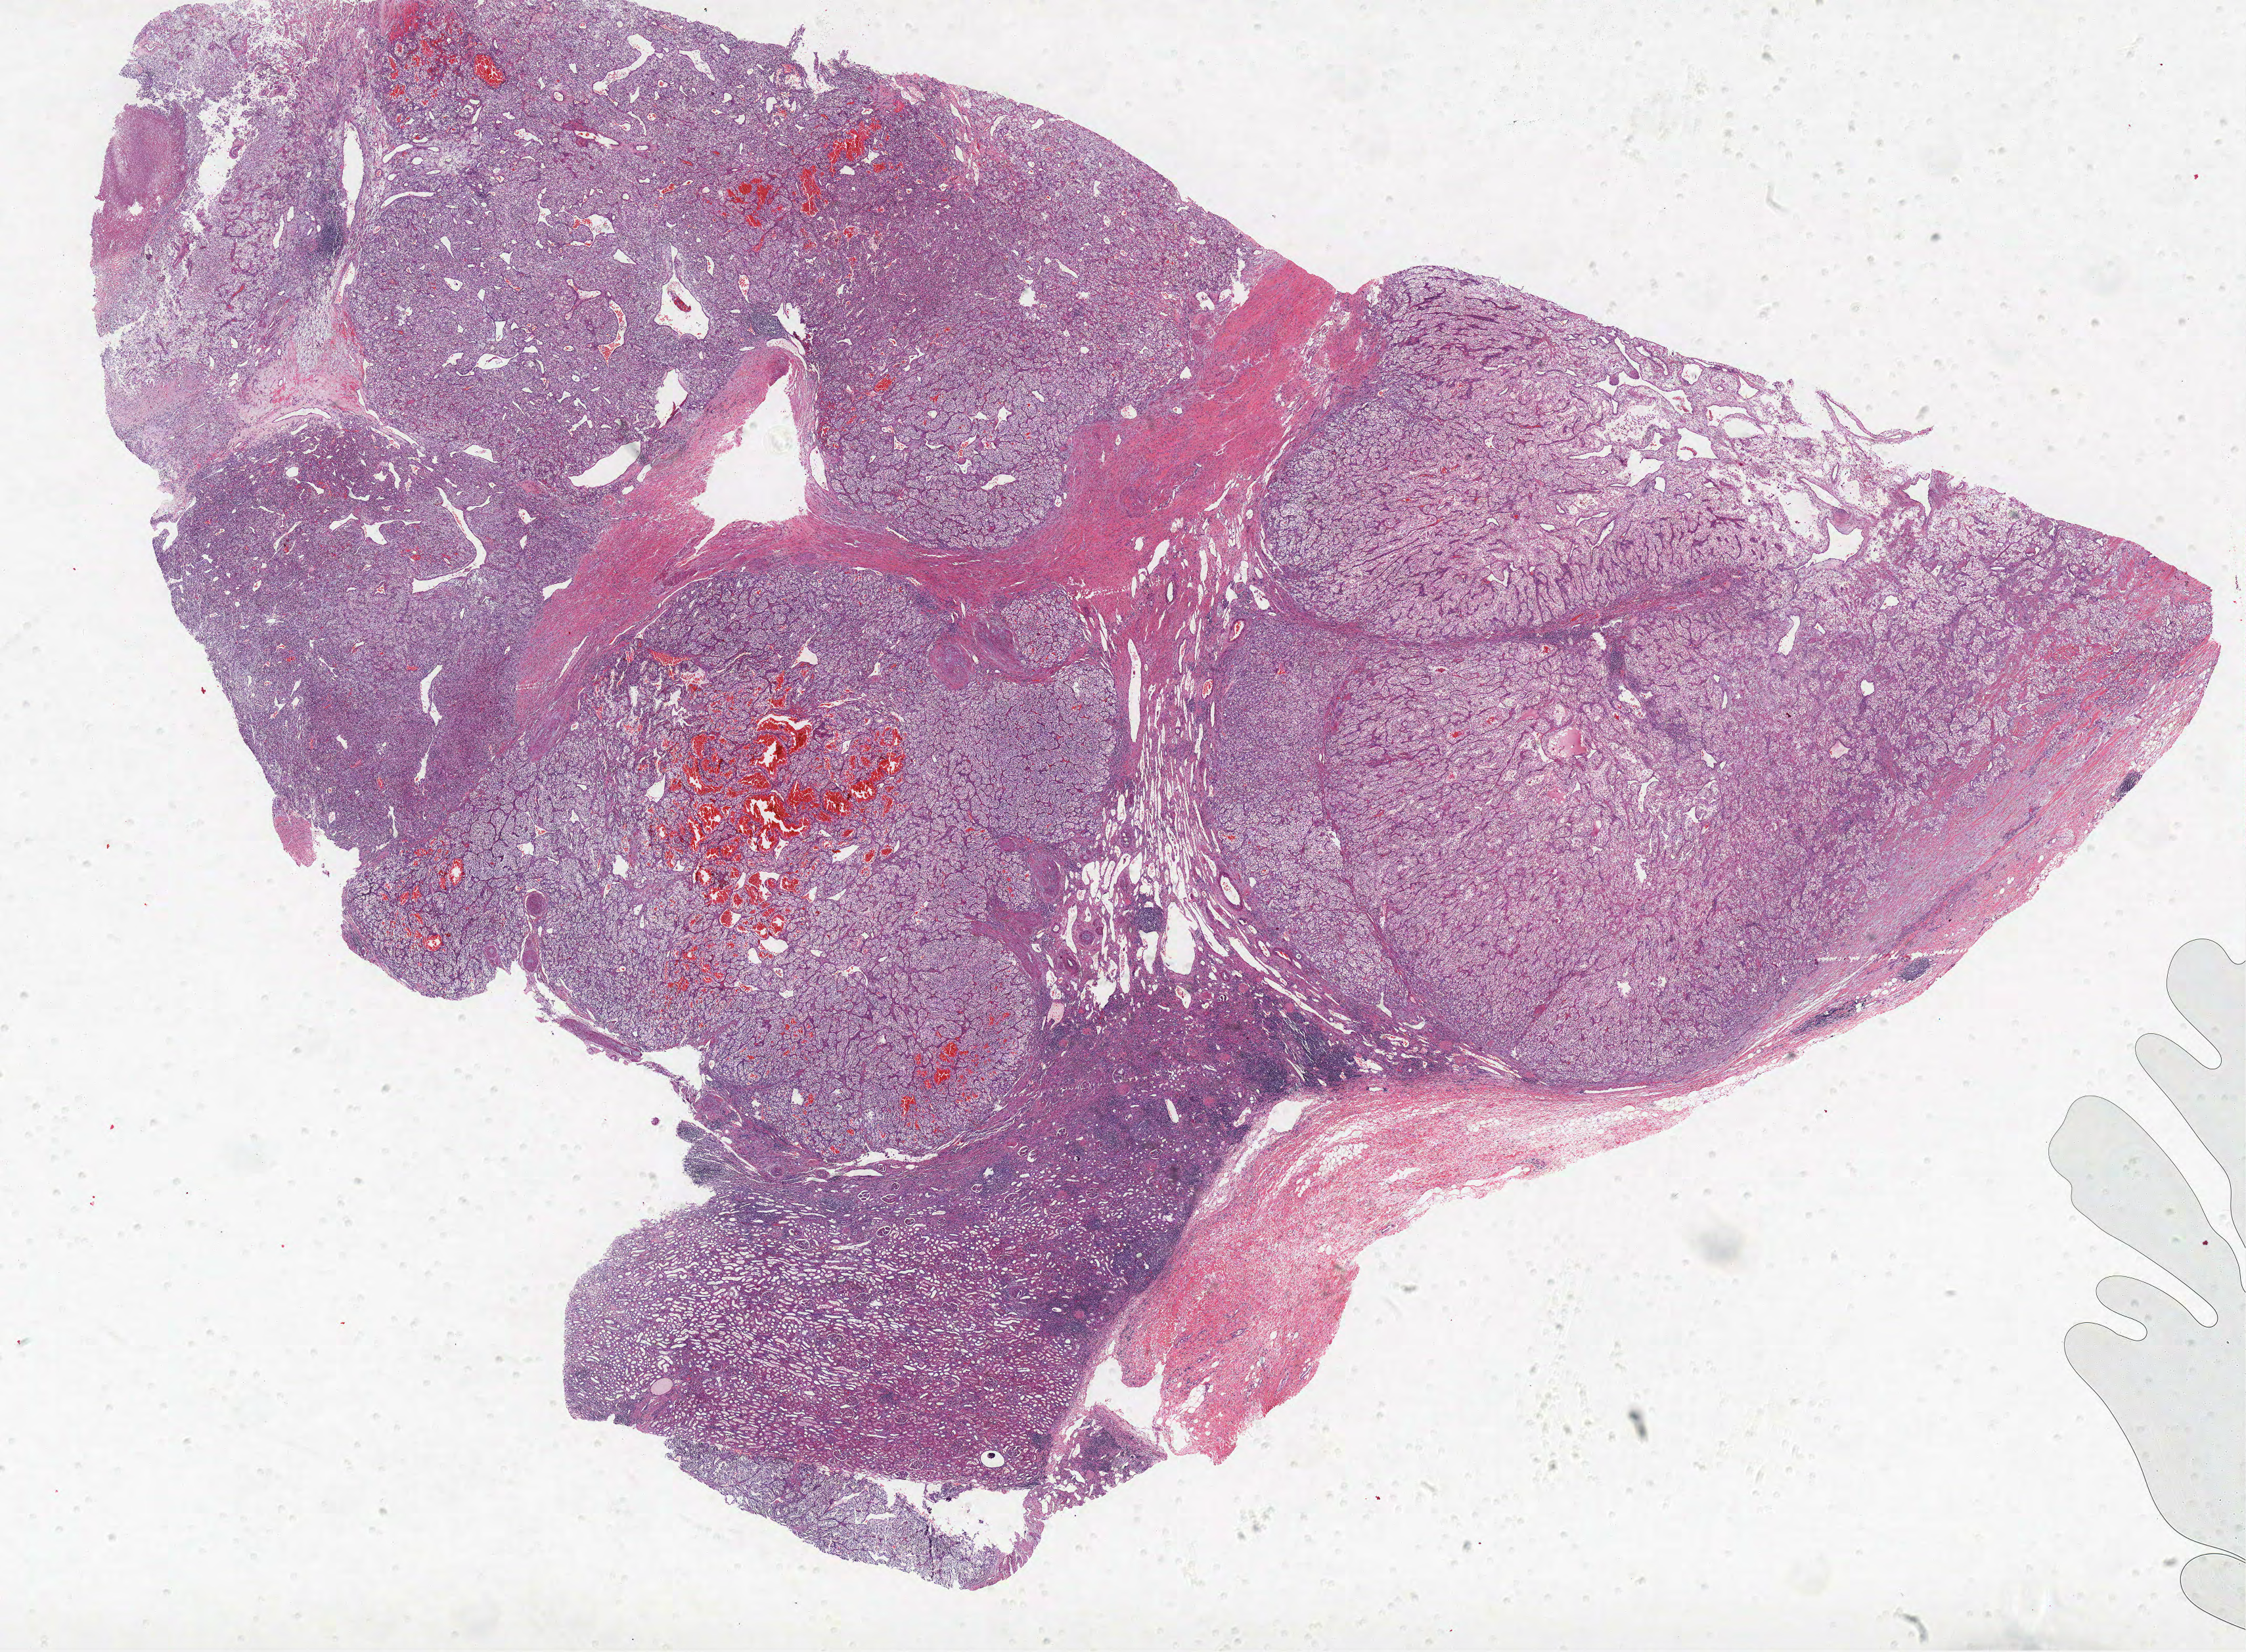
Digitized H&E-stained tissue section (whole slide), whole scanned area (about 27.3 x 20.1 mm) shown as a low-resolution overview, formalin-fixed paraffin-embedded (FFPE) diagnostic section, kidney, primary tumour sample. Male, age 64 years at initial diagnosis. Histologic grade: G3 (poorly differentiated).
• AJCC pathologic stage: III
• diagnosis: Clear cell adenocarcinoma, NOS
• lymph nodes positive (case pathology): 0 of 7 examined
• TNM: T3a N0 M0